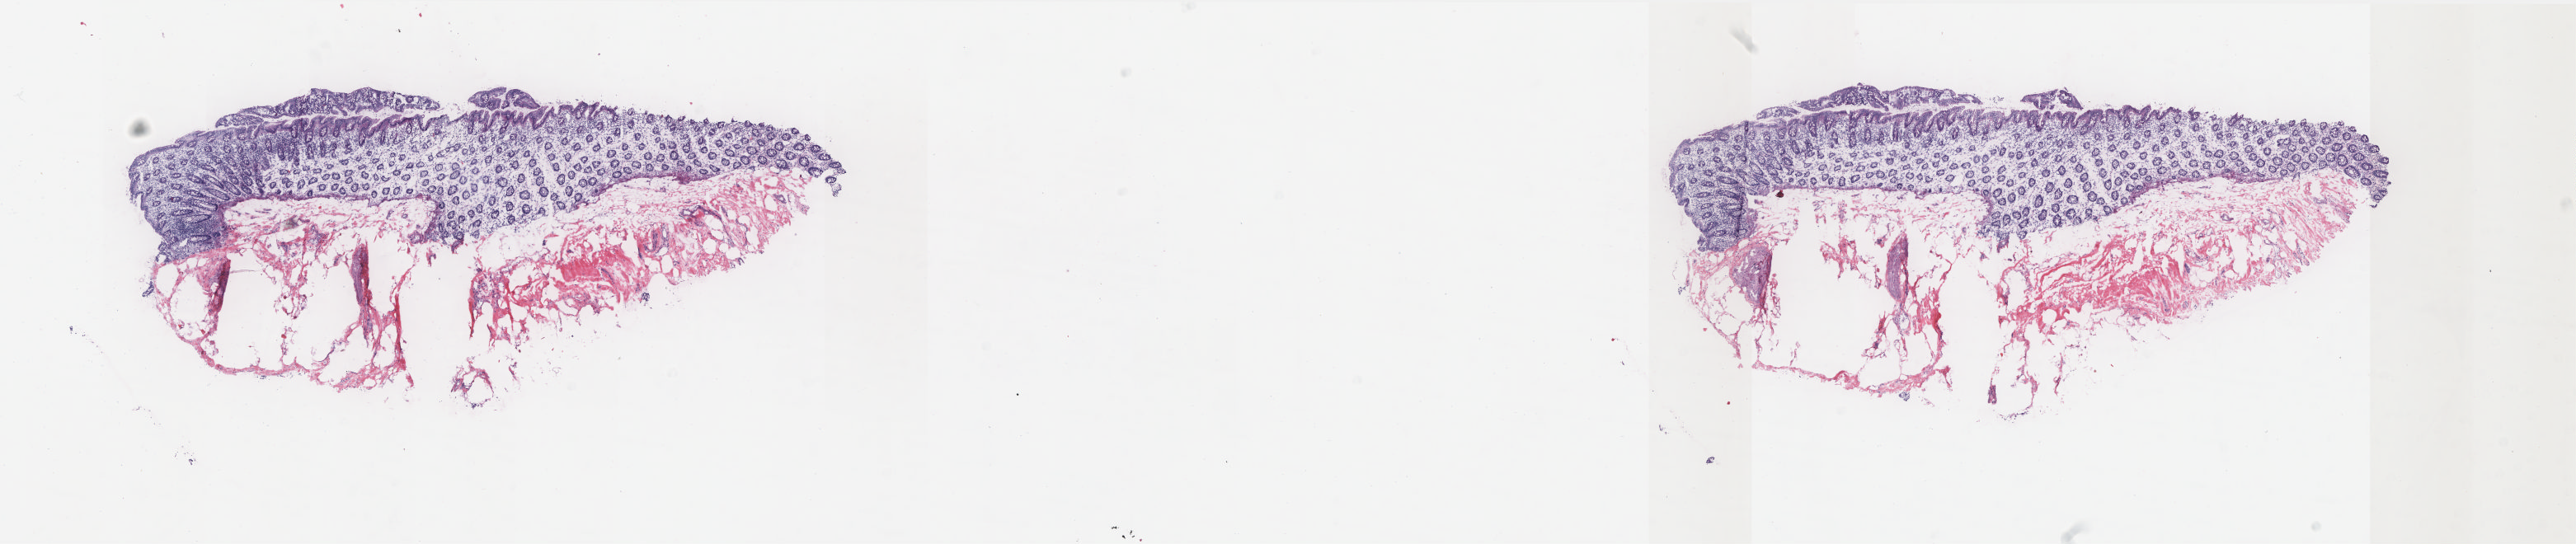
H&E-stained whole-slide image — a low-resolution overview of the entire scanned area, about 25.0 x 5.3 mm (from a 20x scan). Frozen section from the top of the tissue portion. Solid tissue normal (non-tumour tissue) sample from the colon. Patient: male, age at initial diagnosis 59 years. Composition of this section per pathologist review: tumour cells 0%, normal cells 100%. Inflammatory infiltration, as recorded: lymphocyte infiltration 40%, monocyte infiltration 10%, neutrophil infiltration 0%.
This section: solid tissue normal sample (biorepository sample class). Patient diagnosis: Adenocarcinoma, NOS (cecum).